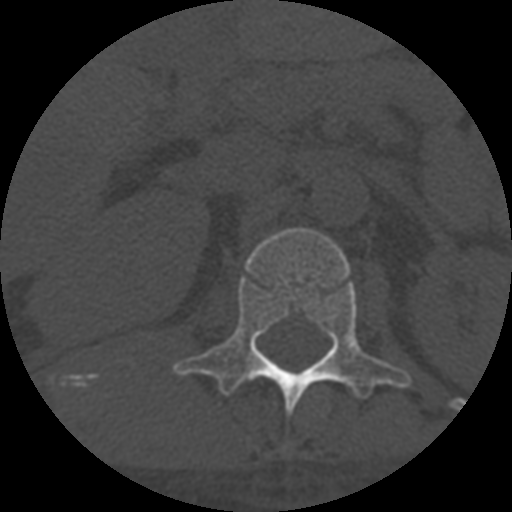
CT including the spine, one axial slice. Slice 289 of 708 in the series (ordered by position). Reconstruction kernel STANDARD. 120 kVp. One of 3 acquisitions stored at this slice position. Bone window (W 1800 / L 400 HU). 1.25 mm slice thickness. 512 × 512 image matrix, field of view 160 × 160 mm. Patient age 55 years. From the clinical record (not read from this slice): primary cancer: colon.
Outlined on this slice (semi-automatically segmented with operator editing):
- L1 vertebra: bounding box [x1, y1, x2, y2] px = [173, 228, 411, 414]